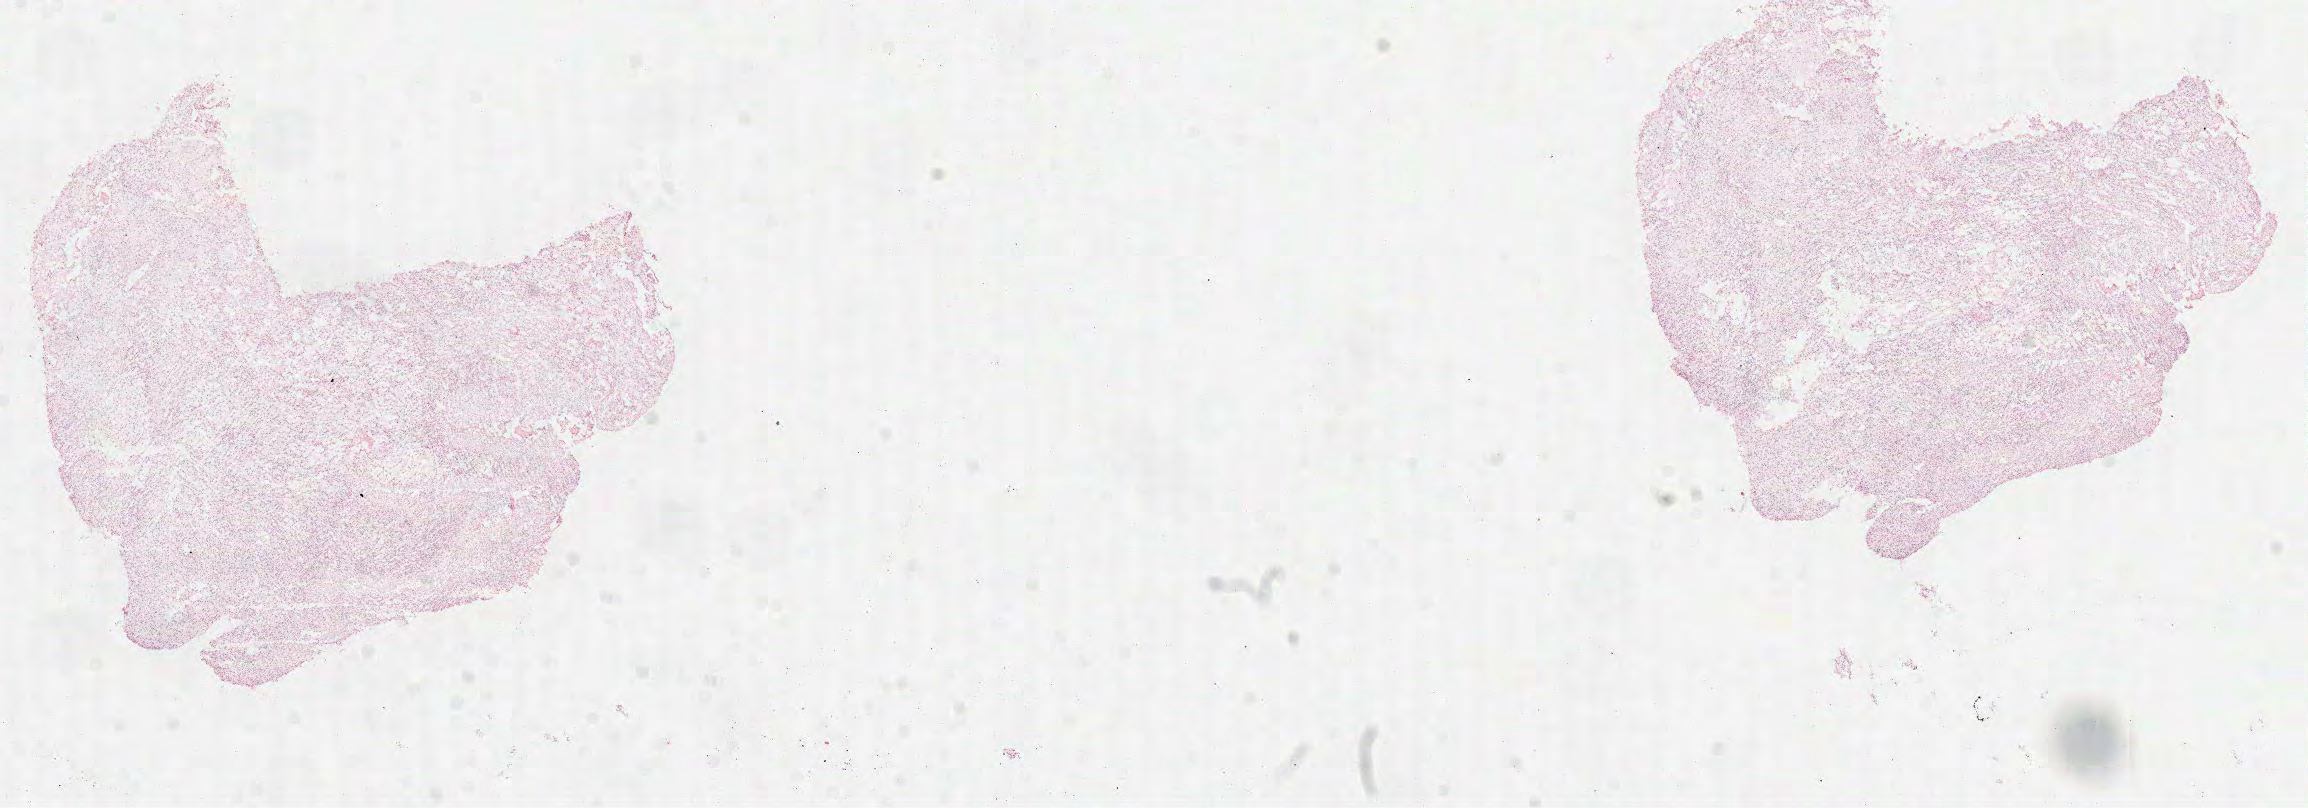
Whole-slide histology image, H&E-stained — low-resolution overview of the scanned area, about 18.6 x 6.5 mm; formalin-fixed paraffin-embedded (FFPE) diagnostic section; primary tumour sample from the brain. Male, age 83 years at initial diagnosis.
Pathologic diagnosis: Glioblastoma.